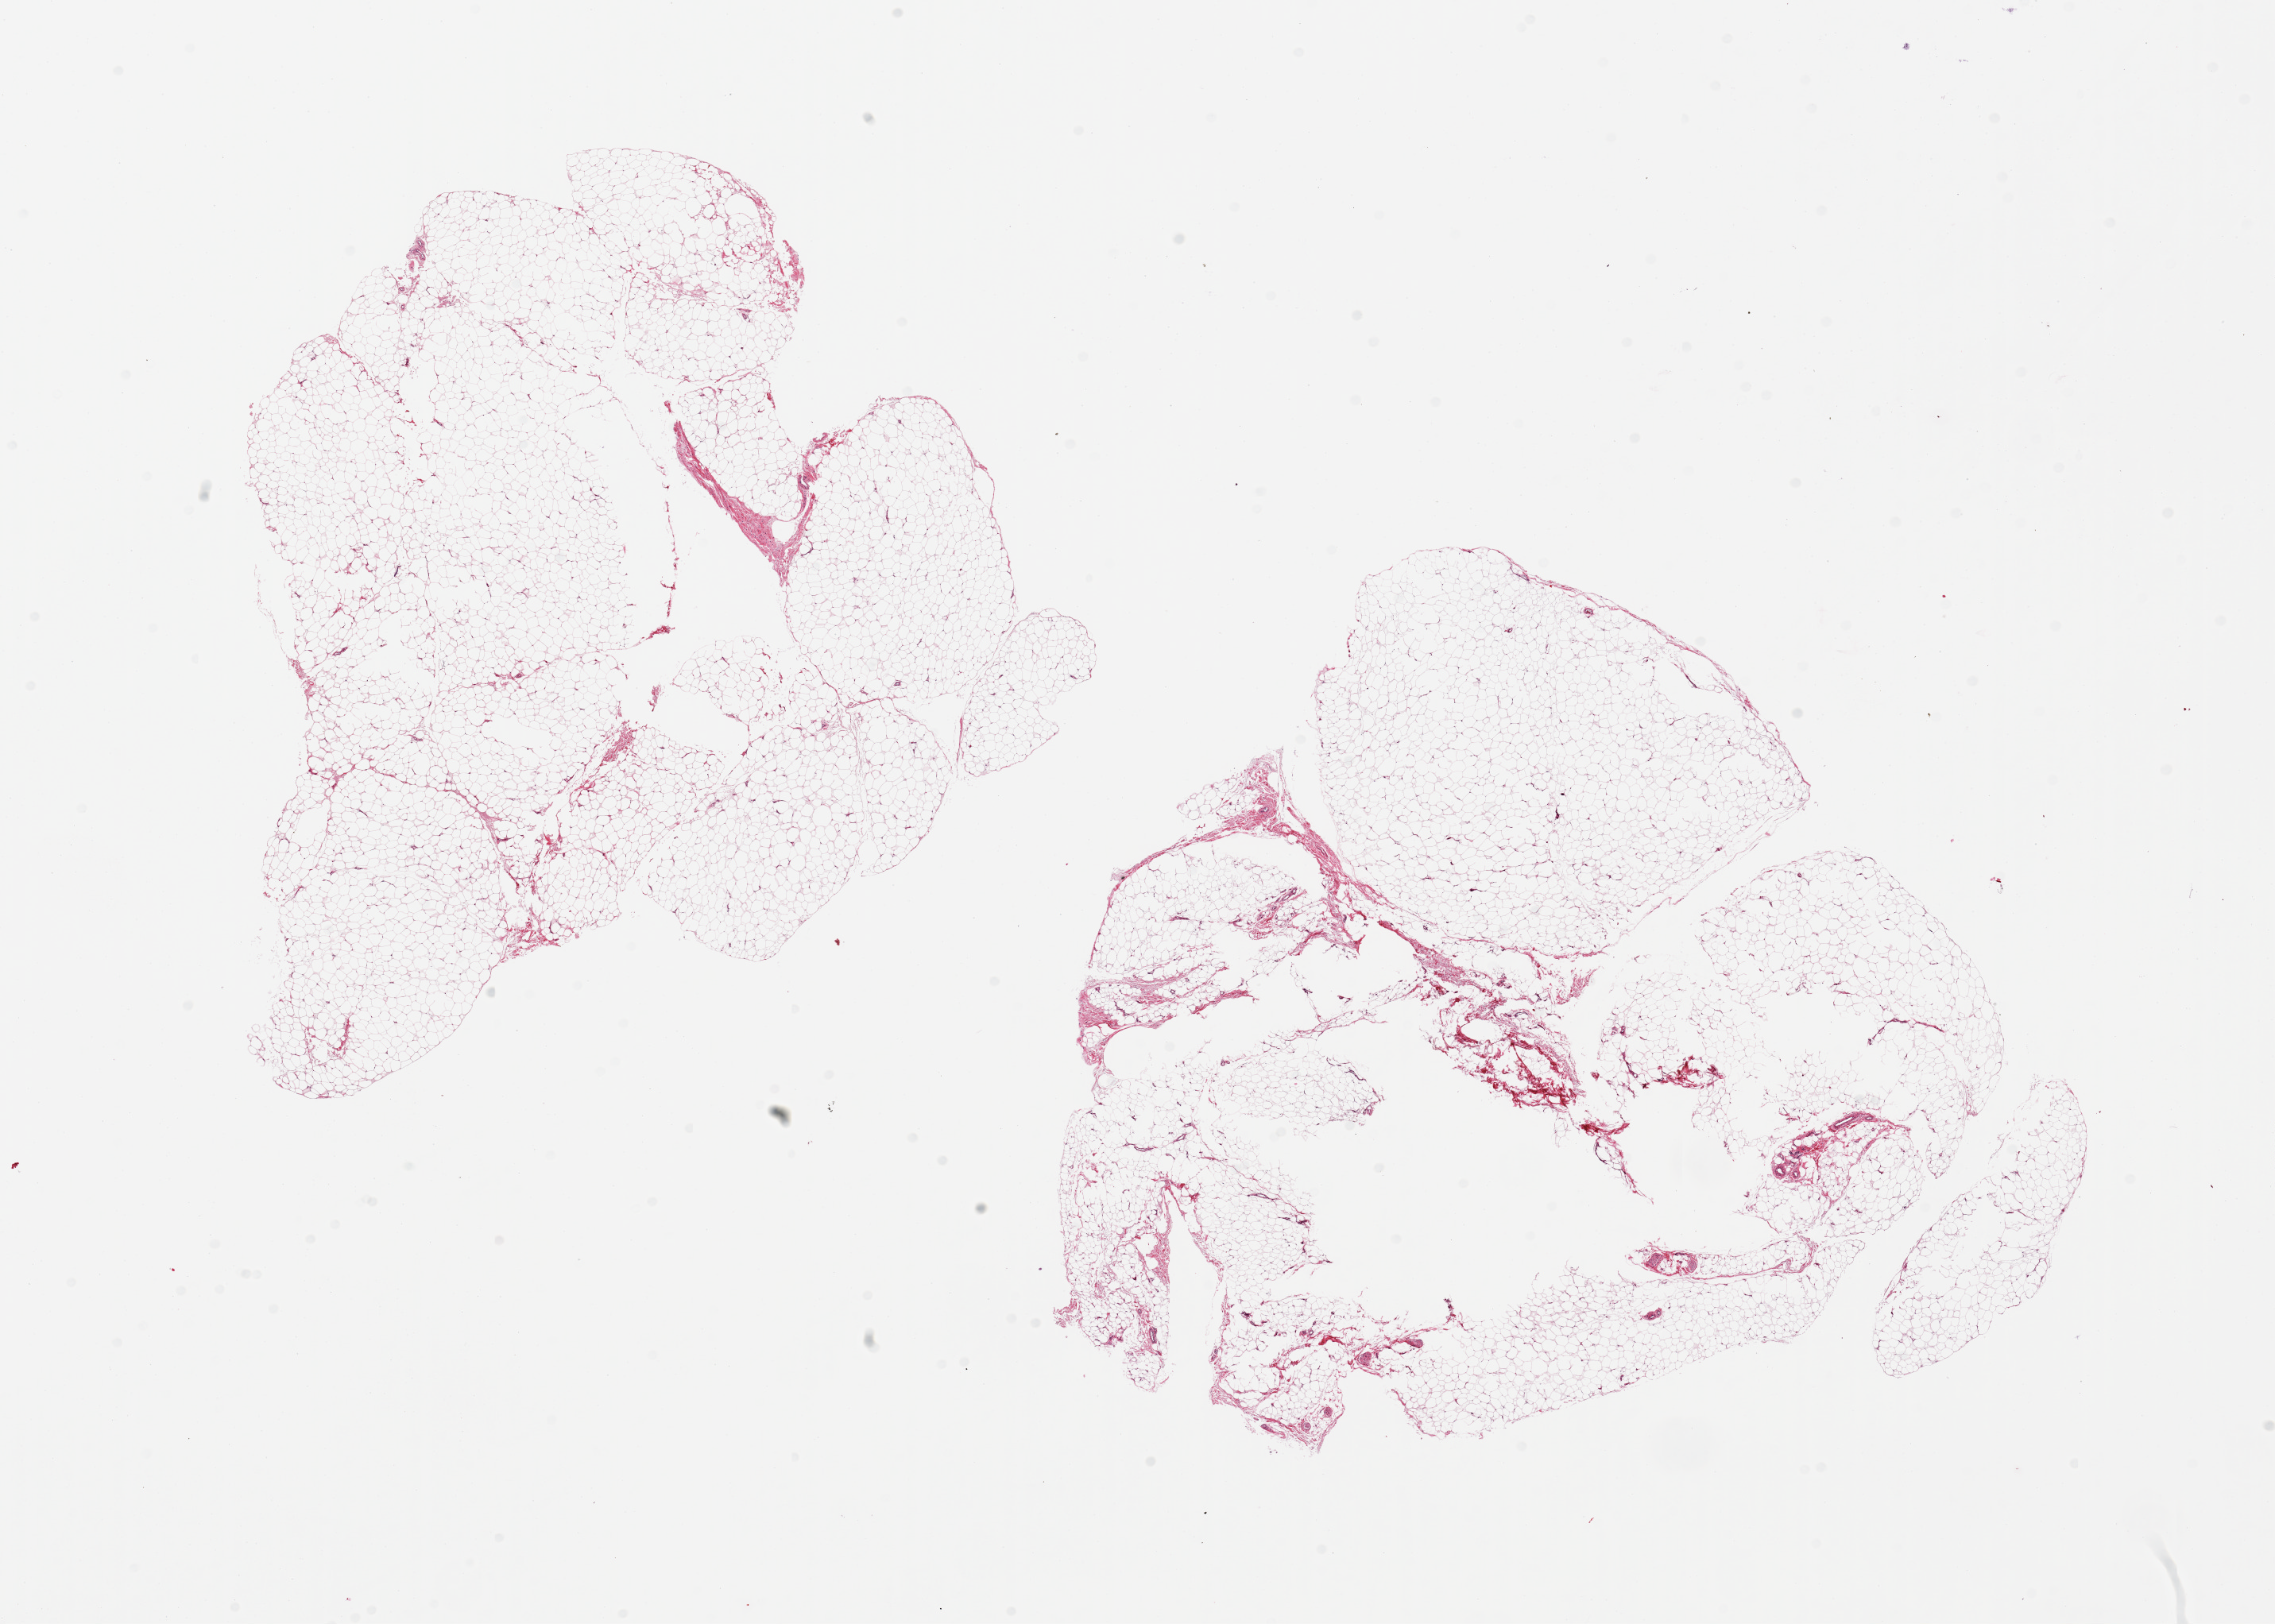
Hematoxylin and eosin (H&E) whole-slide image, shown as a low-resolution overview of the whole scanned area (about 22.6 x 16.2 mm); PAXgene-fixed, paraffin-embedded tissue; section of adipose tissue (target tissue); donor tissue sample. Donor sex: male.
Review note (as recorded): 2 pieces; mature adipose tissue with central defect (?poor fixation).